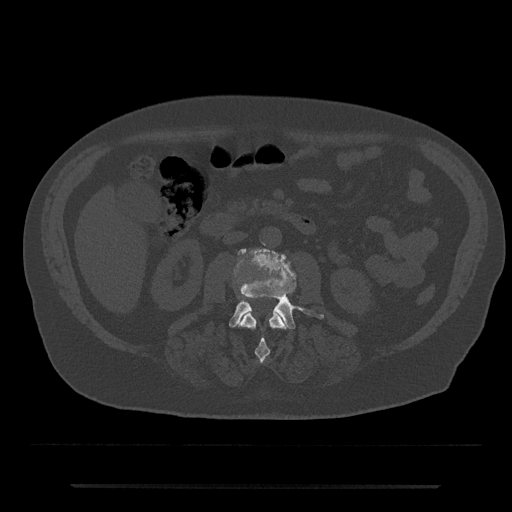
CT including the spine, one axial slice. Position 434 of 797 along the scan axis. Reconstruction kernel Br40s/3. 120 kVp. Bone window (W 1800 / L 400 HU). 512 × 512 image matrix. Male patient, age 80 years. From the clinical record (not read from this slice): primary cancer: prostate.
Structures marked on this image (semi-automatically segmented with operator editing):
- L2 vertebra: bounding box (x1, y1, x2, y2) in pixels: (240, 310, 286, 363)
- L3 vertebra: (229, 248, 324, 329)